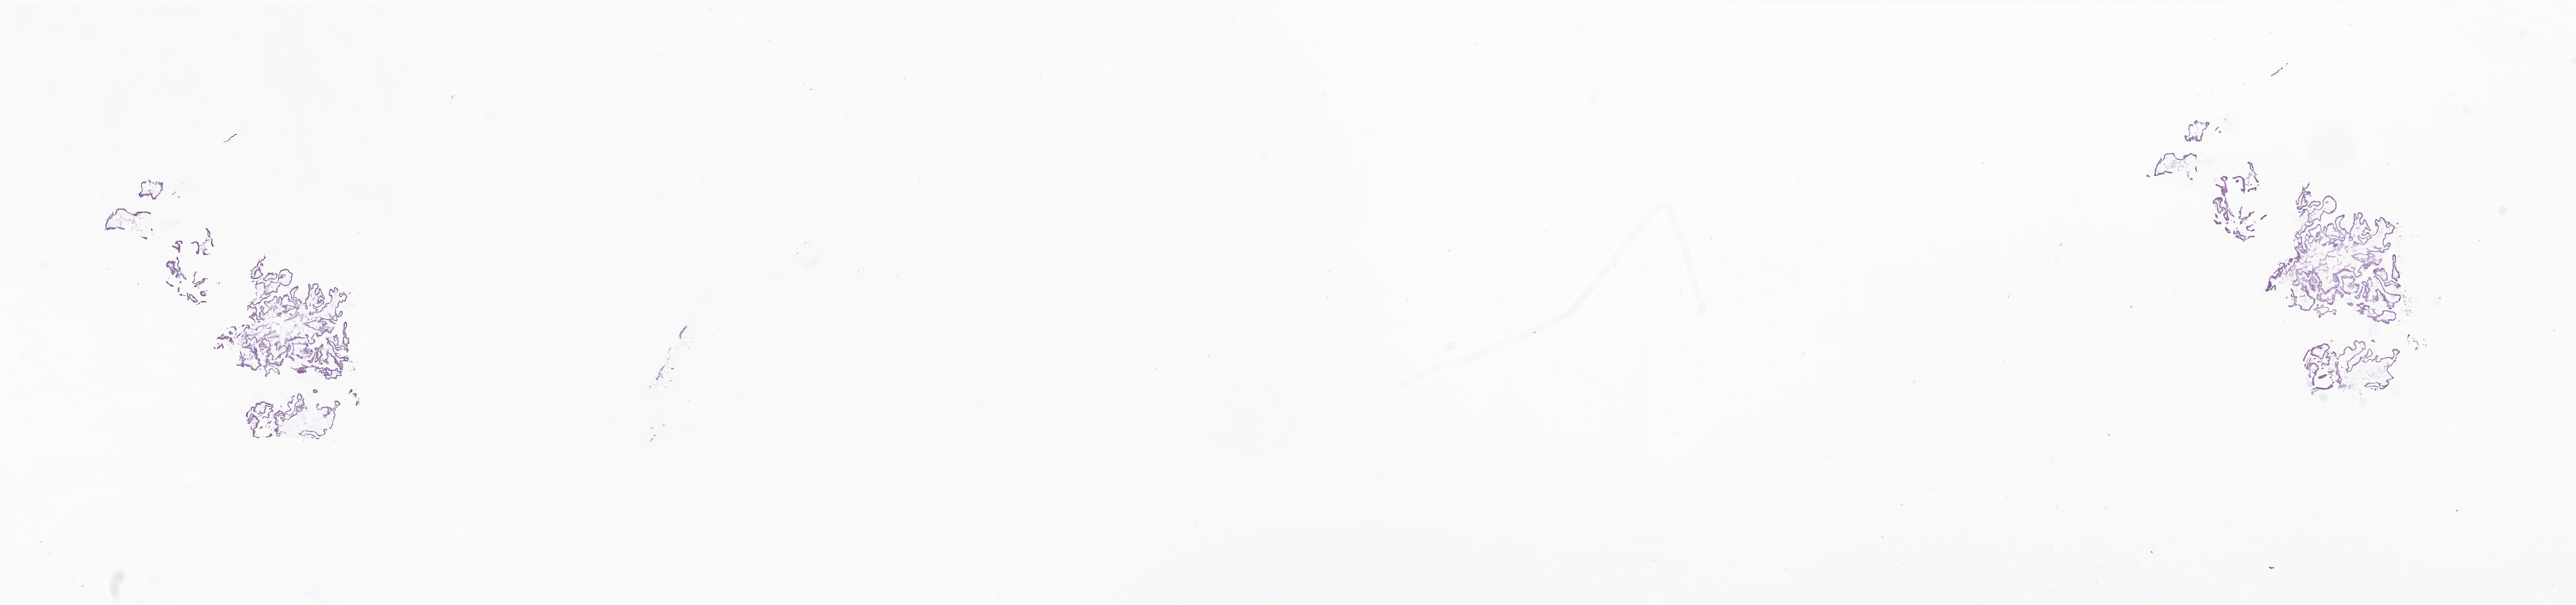
Haematoxylin and eosin whole-slide image of tumor tissue from the brain, whole scanned area (about 28.6 x 6.7 mm) shown as a low-resolution overview, cryosection (OCT / tissue freezing medium). Patient: female, age 50 months (4 years 2 months).
Recorded diagnosis: Choroid plexus papilloma, NOS.